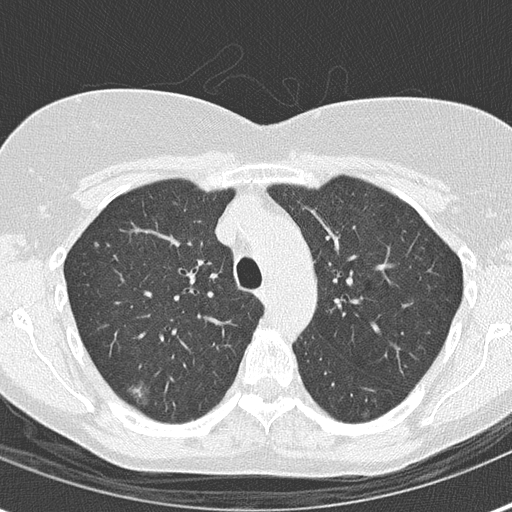
Axial slice from a low-dose chest CT screening exam, baseline screening round, lung window (W 1500 / L -600 HU), lung (sharp) reconstruction kernel (B50f), slice 44 of 147 in the series, 512 × 512 image matrix. Female, age 56 years at enrolment.
Lesion marked by an expert reader, bounding box [x1, y1, x2, y2] px = [111, 366, 160, 419]. The screening reader recorded 2 non-calcified nodules or masses ≥4 mm on this exam (right upper lobe, left upper lobe); which of them this box marks is not recorded.